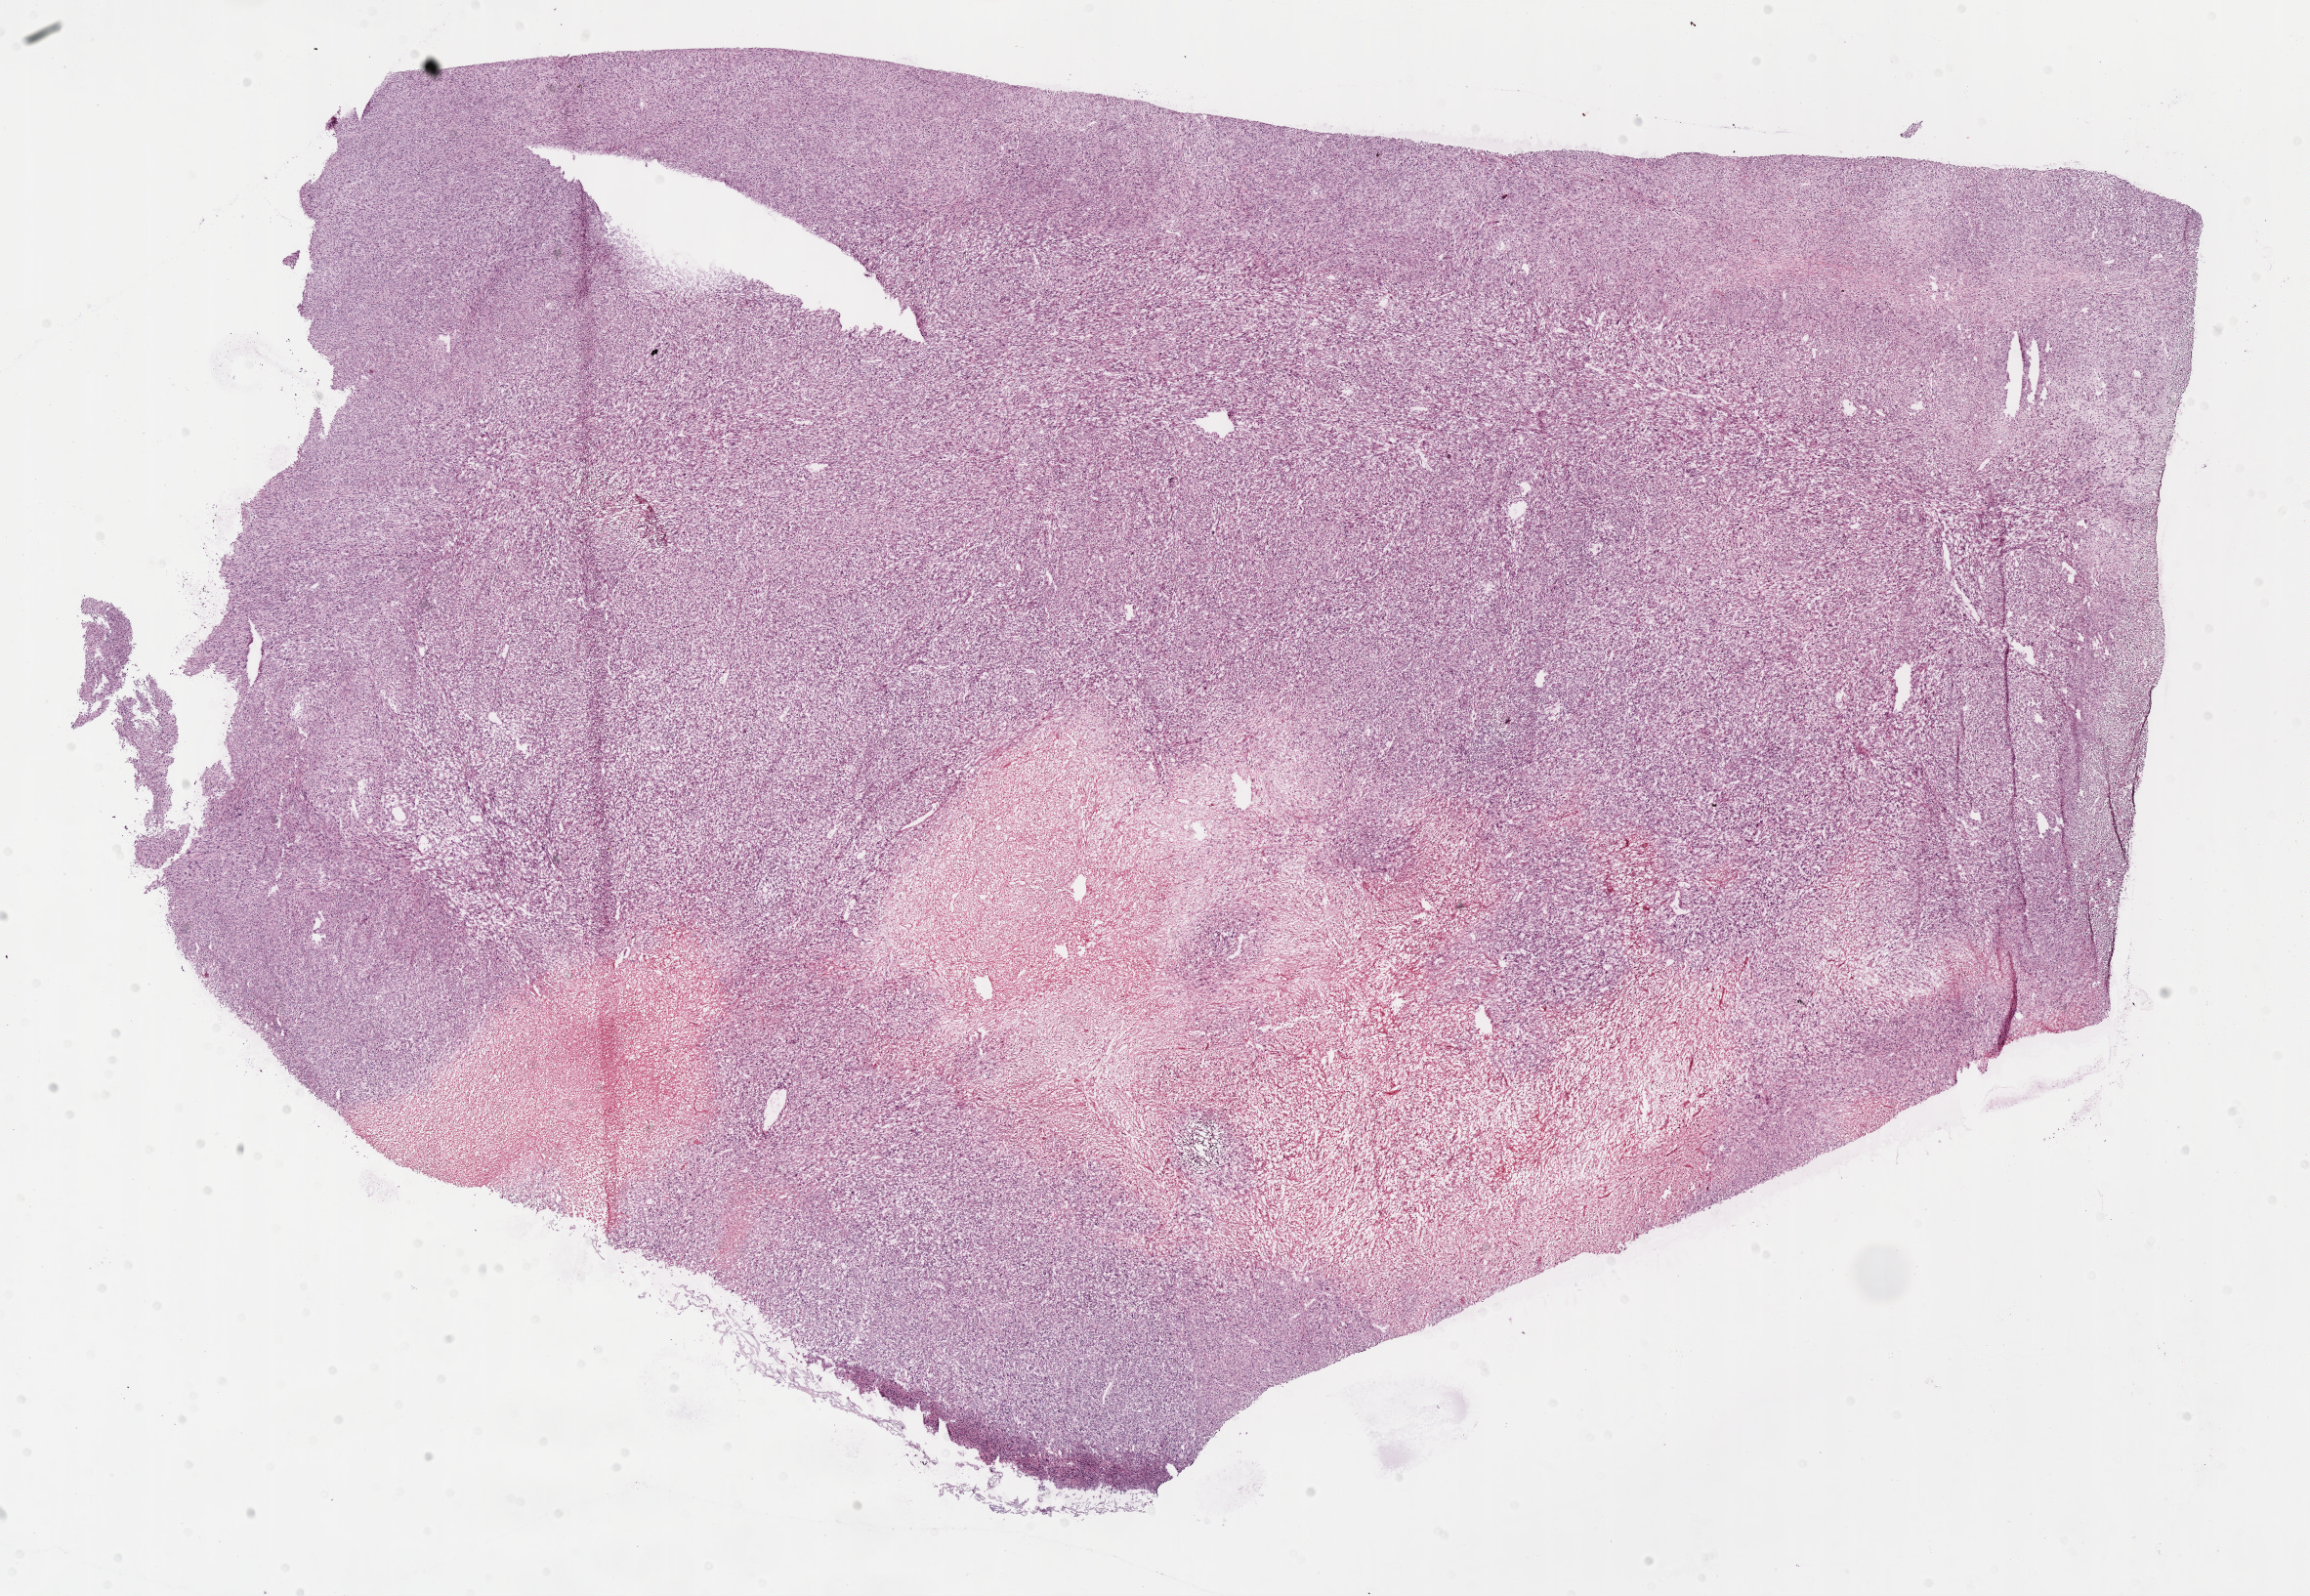
Whole-slide histology image, Hematoxylin and eosin (H&E) stained, low-resolution overview of the scanned area, about 19.1 x 13.2 mm, frozen section from the bottom of the tissue portion, sample: primary tumour, kidney. Male, age 46 years at initial diagnosis. Pathologist review of this section (percent, as recorded): tumour cells 60%, tumour nuclei 85%.
Diagnosis: Clear cell adenocarcinoma, NOS.